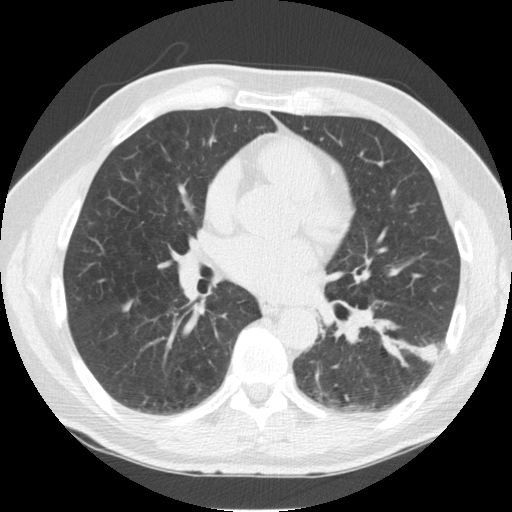
Chest CT (low-dose screening protocol), one axial image. Third screening round (two years after baseline). Lung window (W 1500 / L -600 HU). Slice 72 of 126 in the series. 512 × 512 image matrix. Male, age 57 years at enrolment.
Lesion marked by an expert reader, bounding box (x1, y1, x2, y2) in pixels: (409, 326, 452, 372). Screening reader's record for this exam (one nodule recorded; not confirmed to be the boxed lesion): non-calcified nodule or mass ≥4 mm, left lower lobe, 13 × 12 mm, spiculated (stellate) margins, soft tissue attenuation, pre-existing on the prior screen: yes; interval growth: yes.